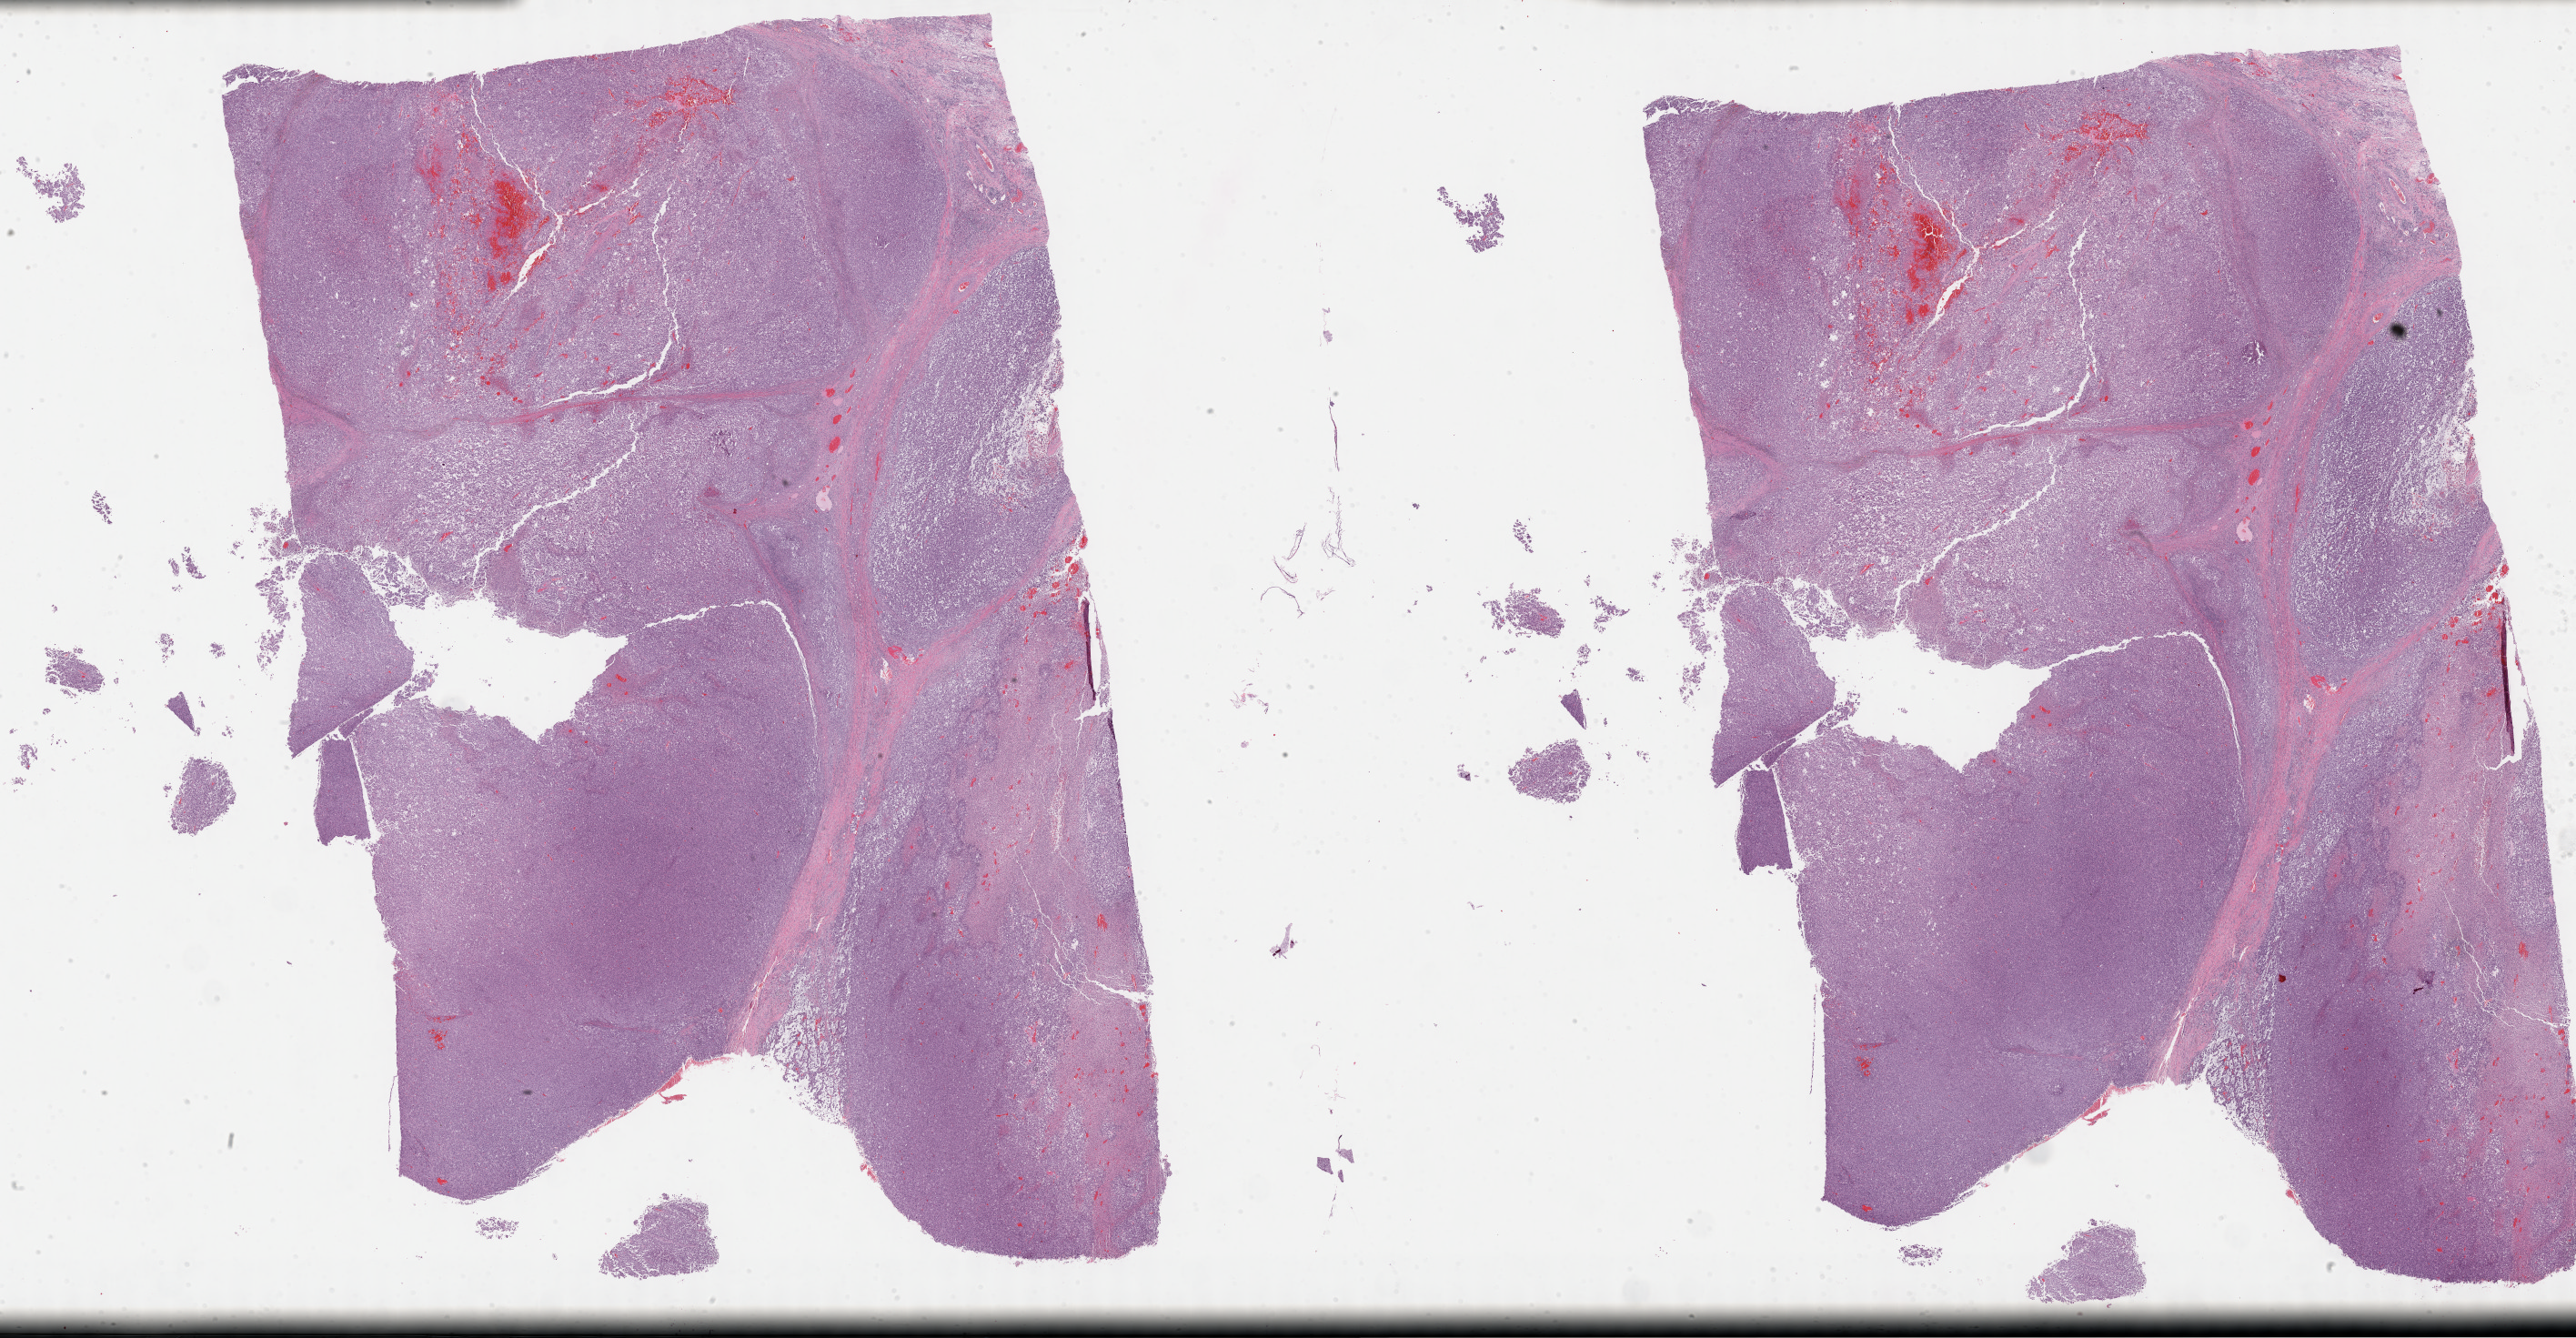
H&E whole-slide image — whole scanned area (about 45.8 x 23.8 mm, acquisition: 40x scan) shown as a low-resolution overview, formalin-fixed paraffin-embedded (FFPE) diagnostic section, connective, subcutaneous and other soft tissues, primary tumour sample. Female patient; age at initial diagnosis 73 years.
Histologic diagnosis: Undifferentiated sarcoma (connective, subcutaneous and other soft tissues of lower limb and hip).